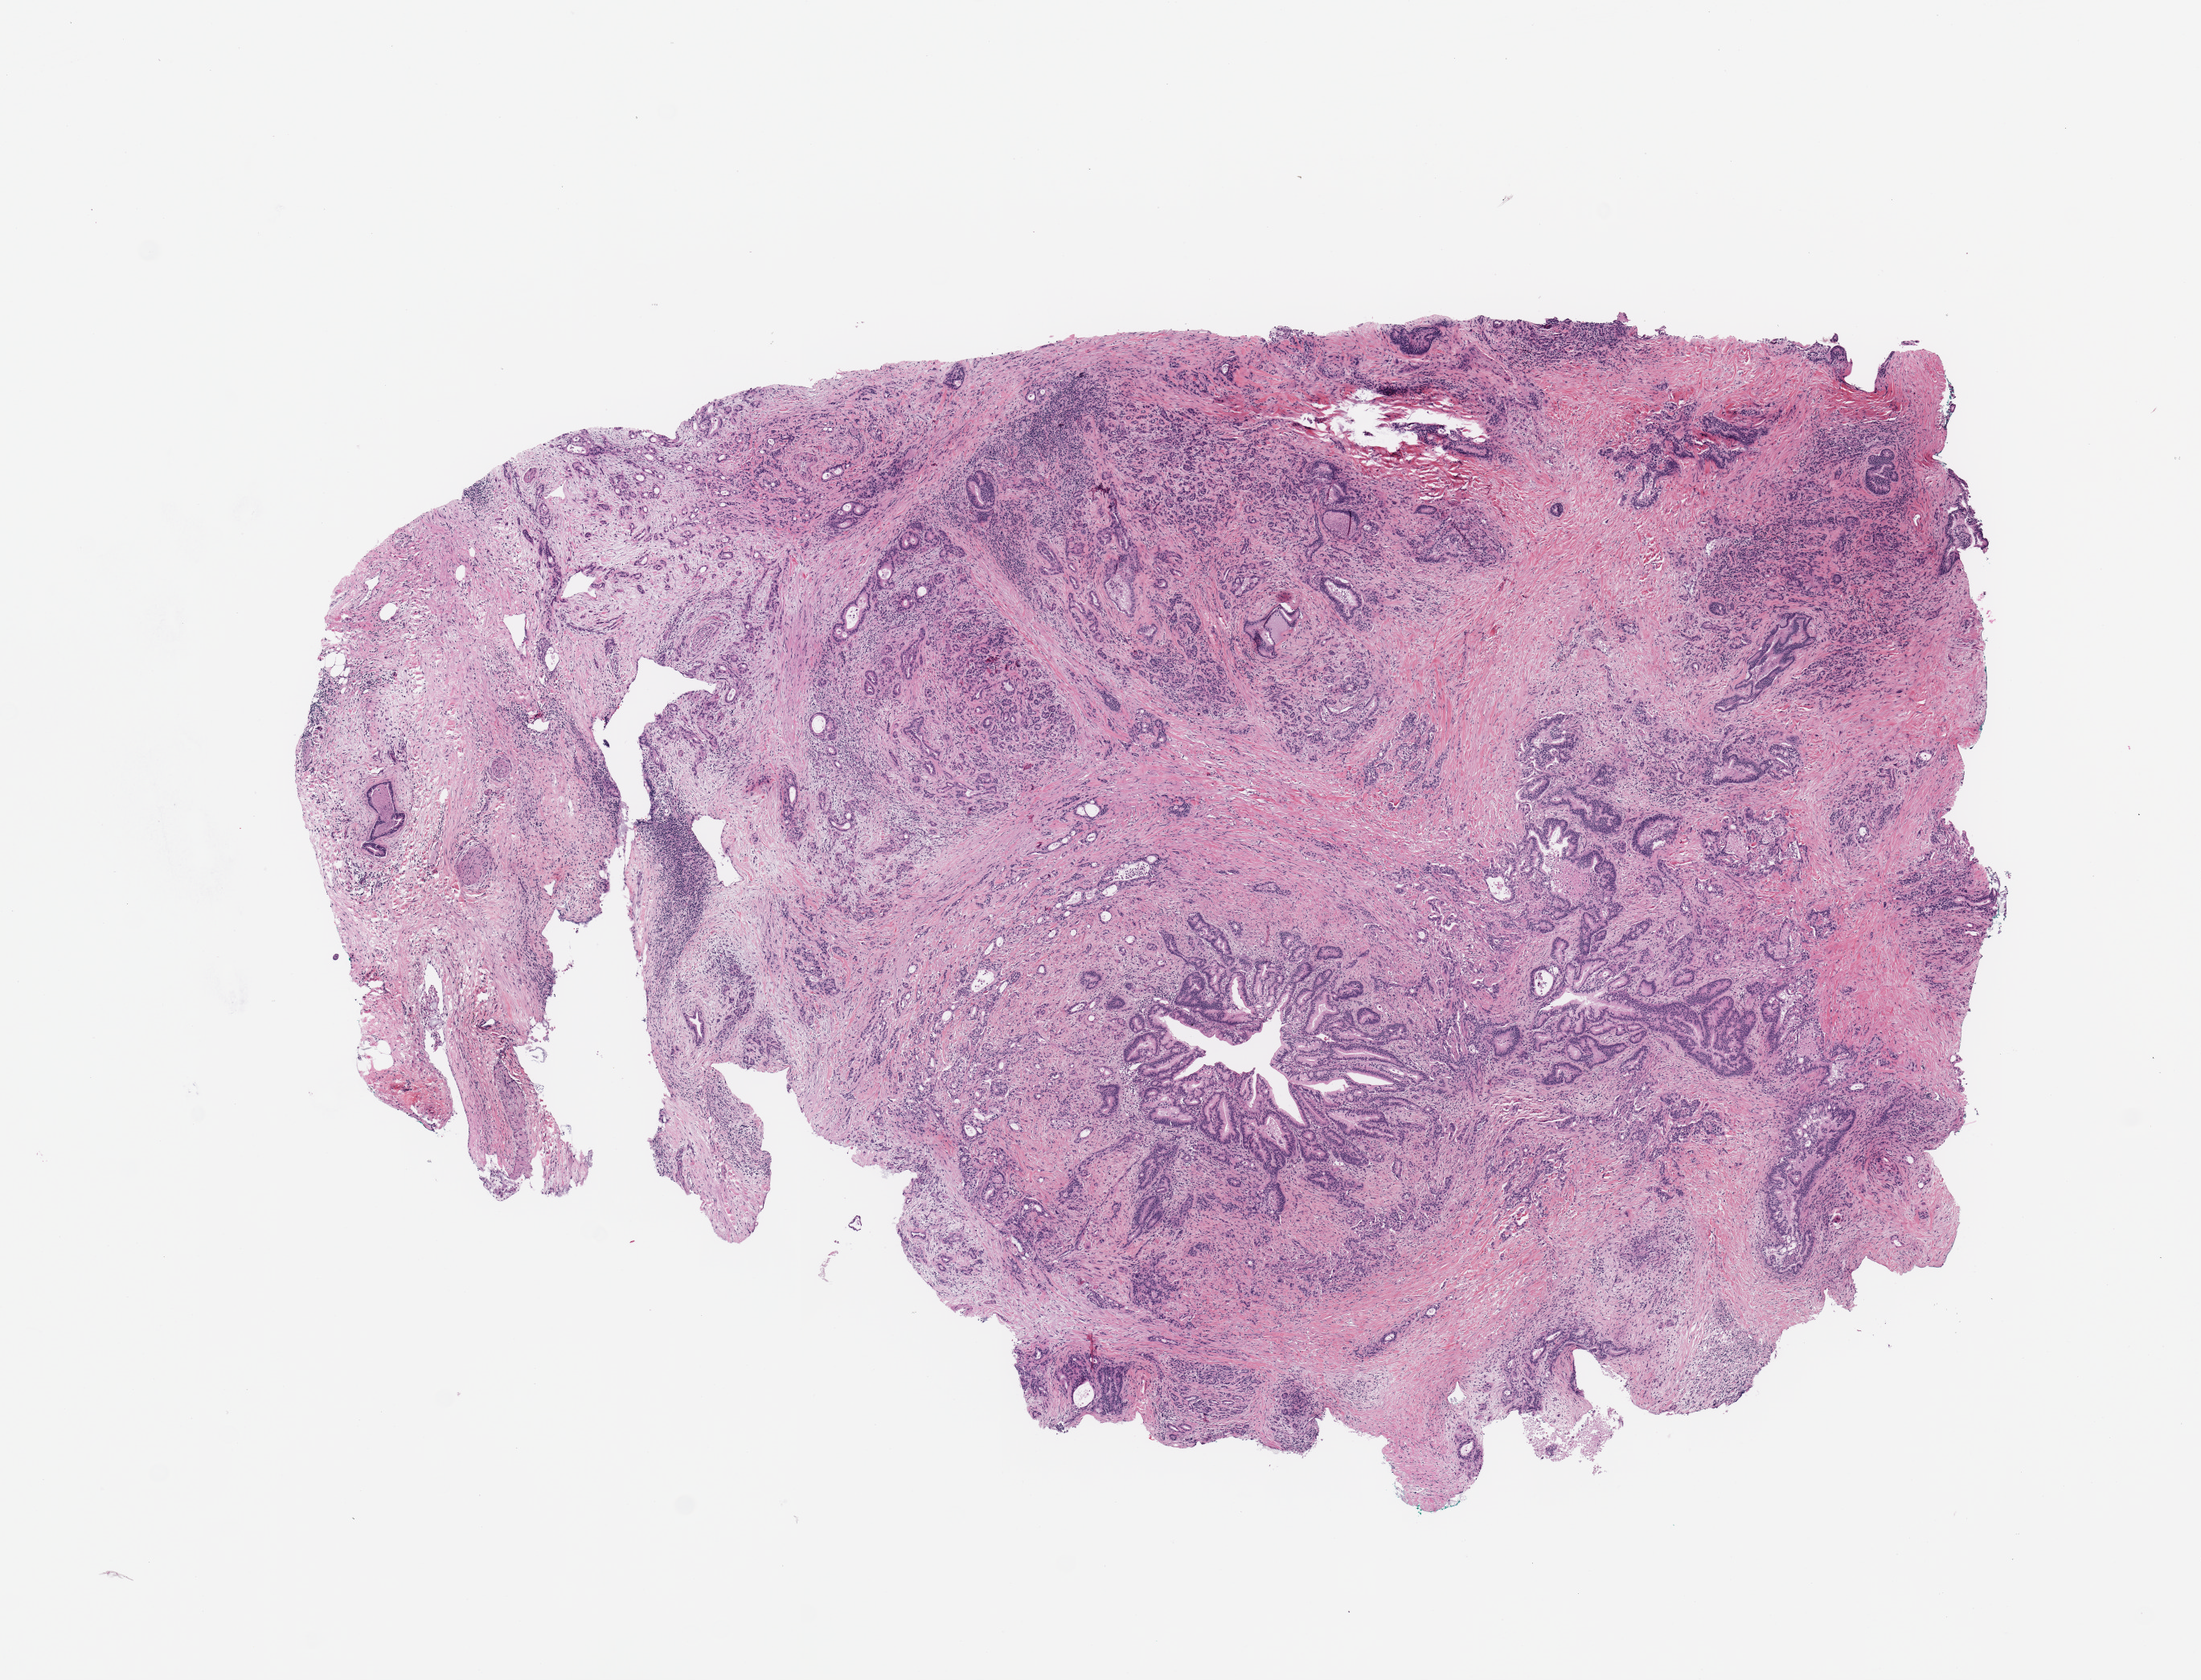
Digitized H&E tissue section (whole slide), a low-resolution overview of the entire scanned area, about 10.8 x 8.3 mm. Tumour tissue sample, sampled site: pancreas. Patient: male, age 64 years. Histologic grade: G2 (moderately differentiated). Slide review estimates, as recorded: tumour nuclei 50%, necrosis 5%.
Primary tumour site (as recorded): head. Diagnosis: Infiltrating duct carcinoma, NOS. AJCC pathologic stage: IIB.